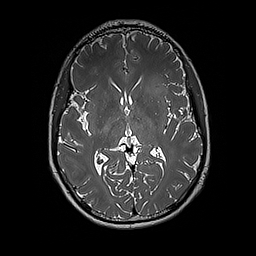
Brain MRI from a brain-tumour surgery series, one axial slice; position 99 of 192 along the scan axis; 1 mm slice thickness; 256 × 256 image matrix, field of view 250 × 250 mm. From the clinical record (not read from this slice): histopathology: Glioblastoma; WHO grade: 4; IDH mutation: no; tumour location: Left Insular.
Structures marked on this image (outlined manually by an expert reader):
- tumour: bounding box [x1, y1, x2, y2] px = [140, 76, 171, 113]